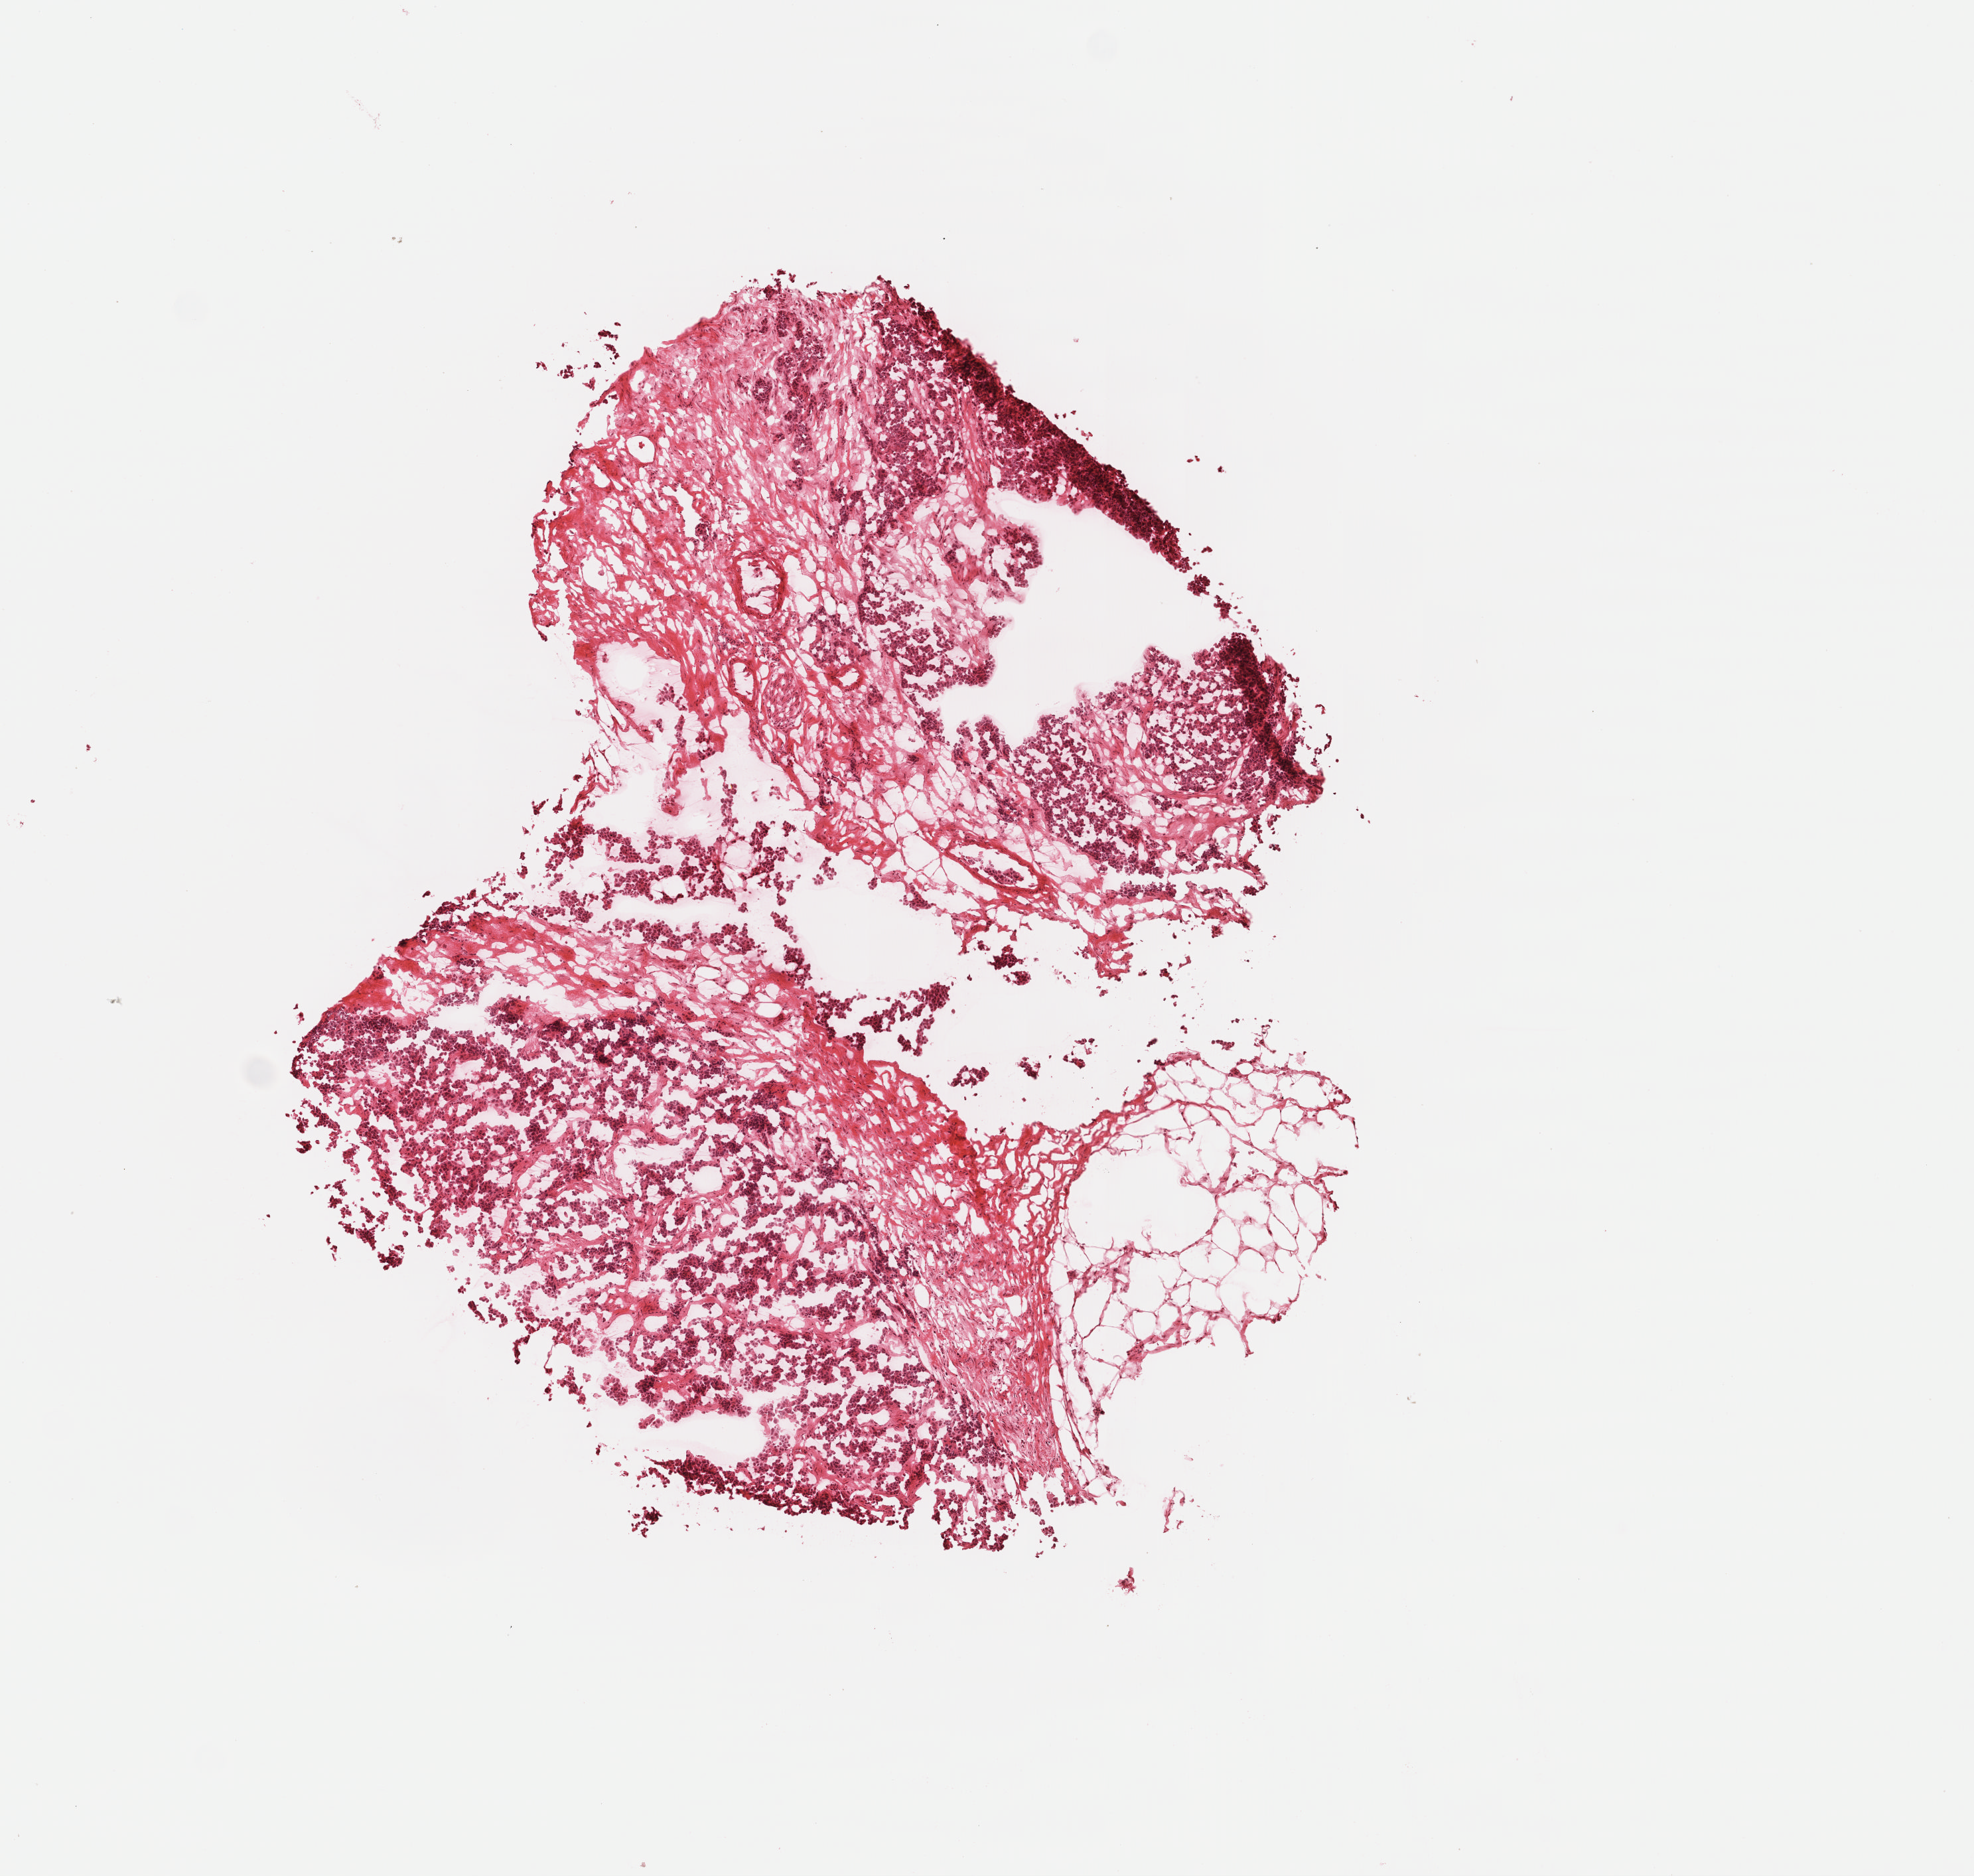
Digitized H&E tissue section (whole slide) — whole scanned area (about 5.8 x 5.6 mm) shown as a low-resolution overview; frozen section from the top of the tissue portion; adrenal cortex, primary tumour sample. Female patient; age at initial diagnosis 71 years. Pathologist review of this section (percent, as recorded): tumour cells 60%, tumour nuclei 65%, normal cells 40%, stromal cells 0%, necrosis 0%. Infiltration values recorded for this section: lymphocyte infiltration 1%, monocyte infiltration 0%, neutrophil infiltration 0%.
Pathologic diagnosis: Adrenal cortical carcinoma (cortex of adrenal gland).